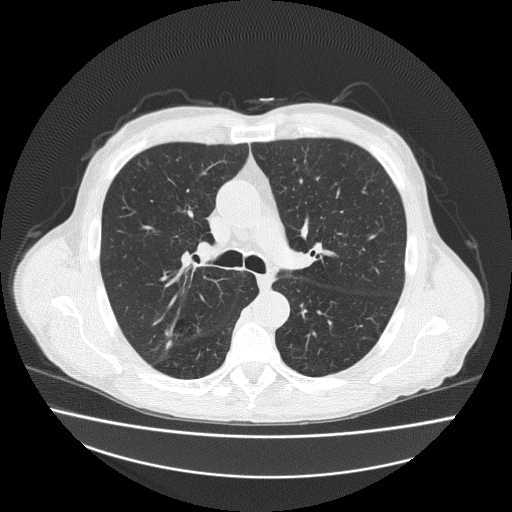
Chest CT (low-dose screening protocol), one axial image, second screening round (one year after baseline), lung window (W 1500 / L -600 HU), 2 mm slice thickness, lung (sharp) reconstruction kernel (FC51), slice 75 of 186 in the series, 512 × 512 image matrix, field of view 408 × 408 mm. Male, age 73 years at enrolment.
- Expert reader's lesion annotation, box from (x=153, y=310) to (x=207, y=349) px.
- Screening reader's record for this exam: no non-calcified nodule ≥4 mm recorded.
- Participant outcome: lung cancer diagnosed 418 days after this screen (after the third annual screen) — adenosquamous carcinoma, right upper lobe, well differentiated (G1), stage IA (AJCC 6th edition), 20 mm at pathology.